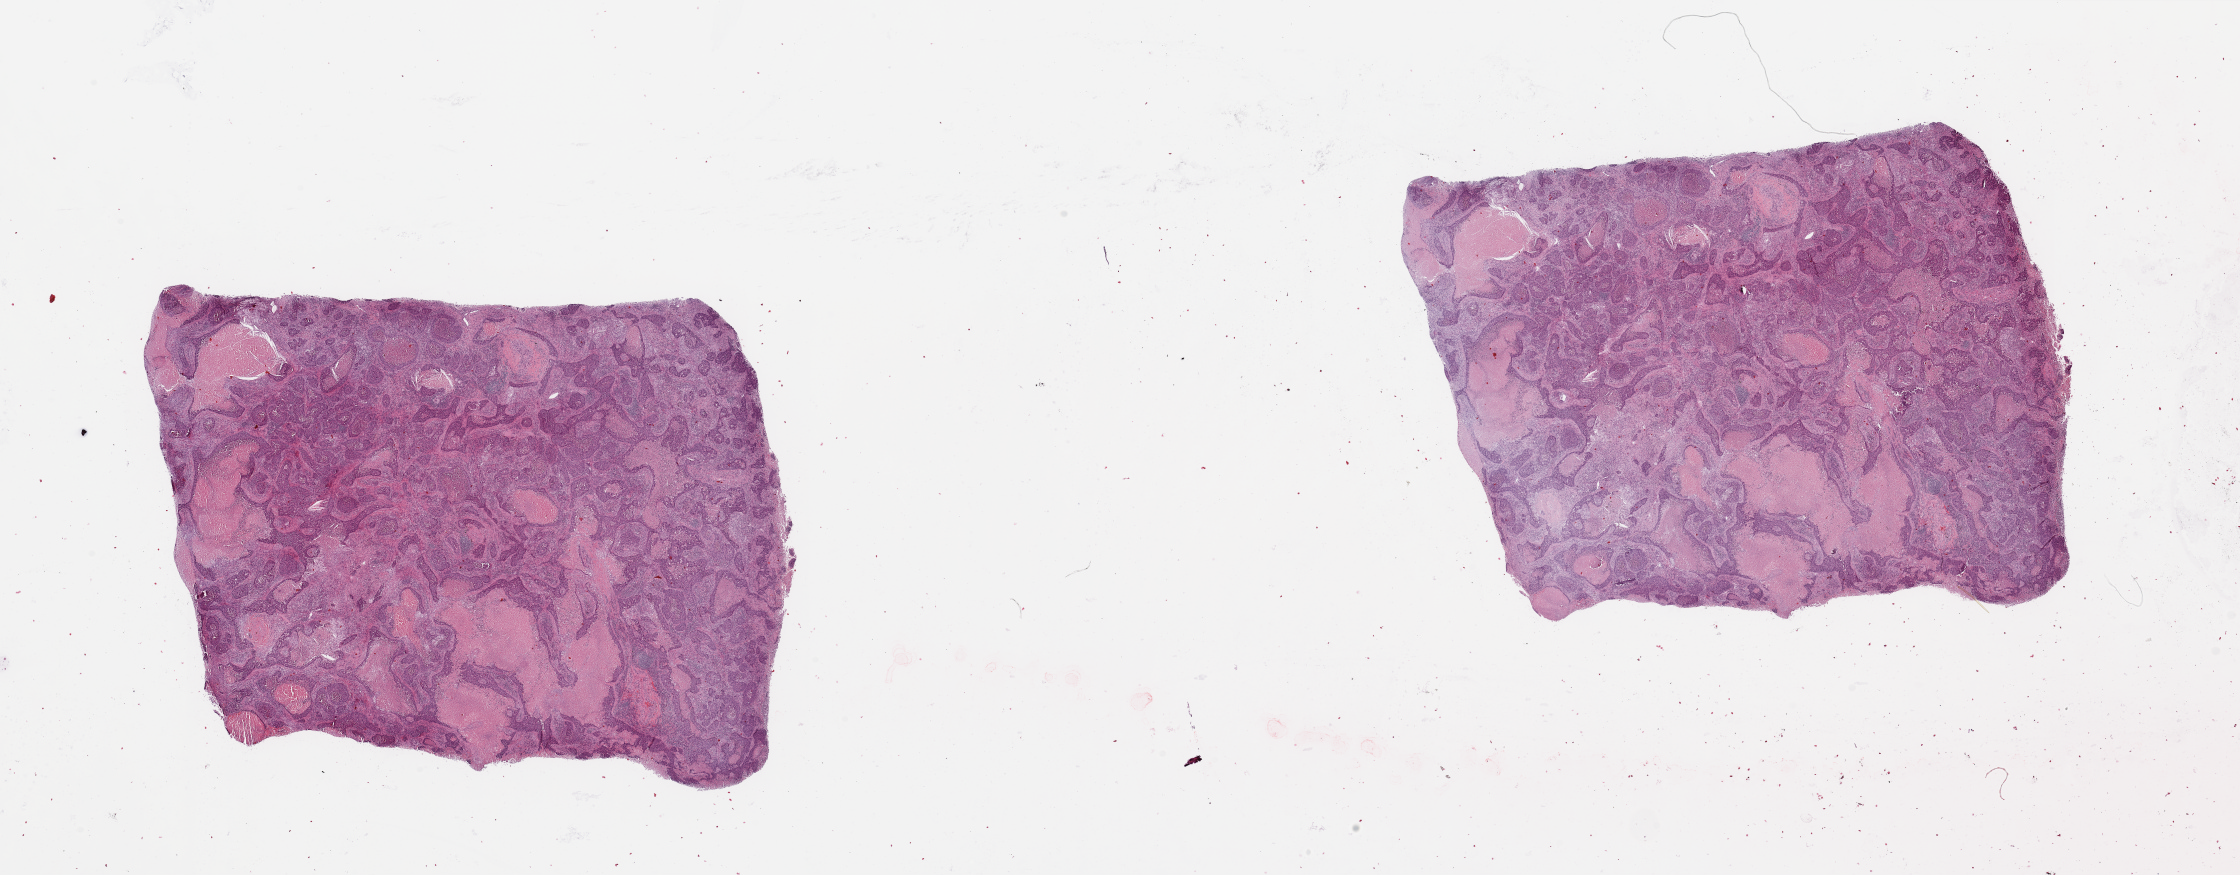
H&E whole-slide image — shown as a low-resolution overview of the whole scanned area (about 35.4 x 13.8 mm, slide scanned at 20x). Tumour tissue sample, lung. Patient: male, age 62 years. Histologic grade: G3 (poorly differentiated).
Diagnosis: Squamous cell carcinoma, NOS. AJCC pathologic stage: IIIB. Primary tumour site (as recorded): left lower lobe.